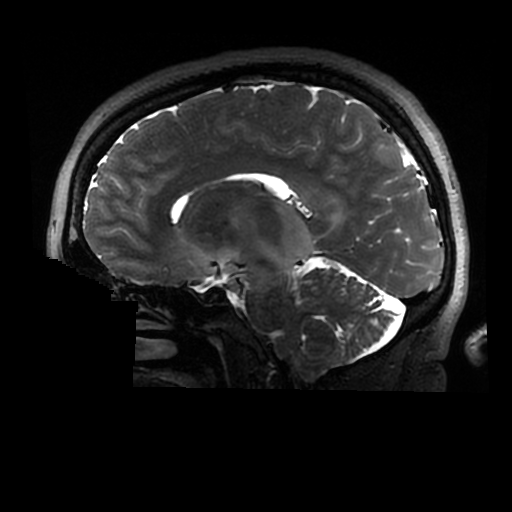
Brain MRI from a brain-tumour surgery series, one sagittal slice. Slice 170 of 320 in the series (ordered by position). 0.6 mm slice thickness. 512 × 512 image matrix. Case-level facts recorded for this patient, not image findings: histopathology: Astrocytoma; WHO grade: 2; IDH mutation: yes.
Annotated regions visible in this slice (outlined manually by an expert reader):
- tumour: box from (x=202, y=202) to (x=315, y=290) px